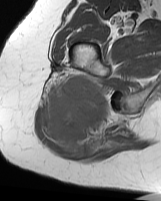
MRI of an extremity soft-tissue mass, one axial slice. Position 42 of 70 along the scan axis. MR volume resampled by the dataset authors to the PET/CT grid (not the native acquisition matrix). 3.27 mm slice thickness. 161 × 201 image matrix, field of view 157 × 196 mm. Female patient. Case-level facts recorded for this patient, not image findings: histological type: synovial sarcoma; grade: intermediate; site of the primary tumour: right buttock.
Outlined on this slice (expert contour drawn on MRI and transferred to this co-registered scan by the dataset authors):
- gross tumour volume including surrounding oedema: bounding box [x1, y1, x2, y2] px = [47, 74, 109, 157]
- gross tumour volume (mass): [47, 74, 109, 146]